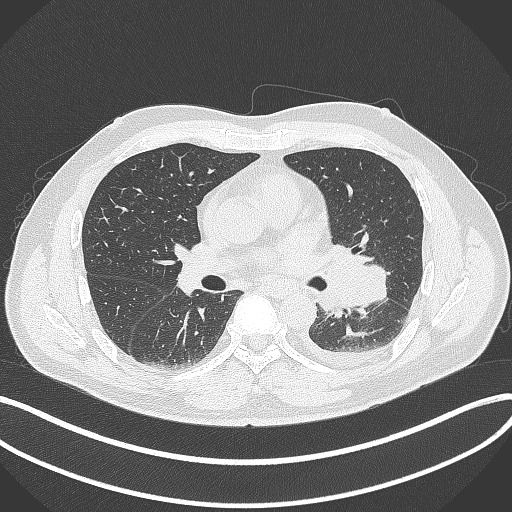
Chest CT, one axial slice; slice 193 of 342 in the series (ordered by position); reconstruction kernel B70f; 120 kVp; lung window (W 1500 / L -600 HU); 1 mm slice thickness; 512 × 512 image matrix, field of view 400 × 400 mm. Patient: male, 58 years. Case-level facts recorded for this patient, not image findings: clinical TNM (as recorded): T3 N1 M1b; histopathological grade: G3.
Structures marked on this image (bounding box drawn by a radiologist):
- lung tumour (recorded histology: small cell carcinoma): bounding box [x1, y1, x2, y2] px = [319, 239, 390, 318]